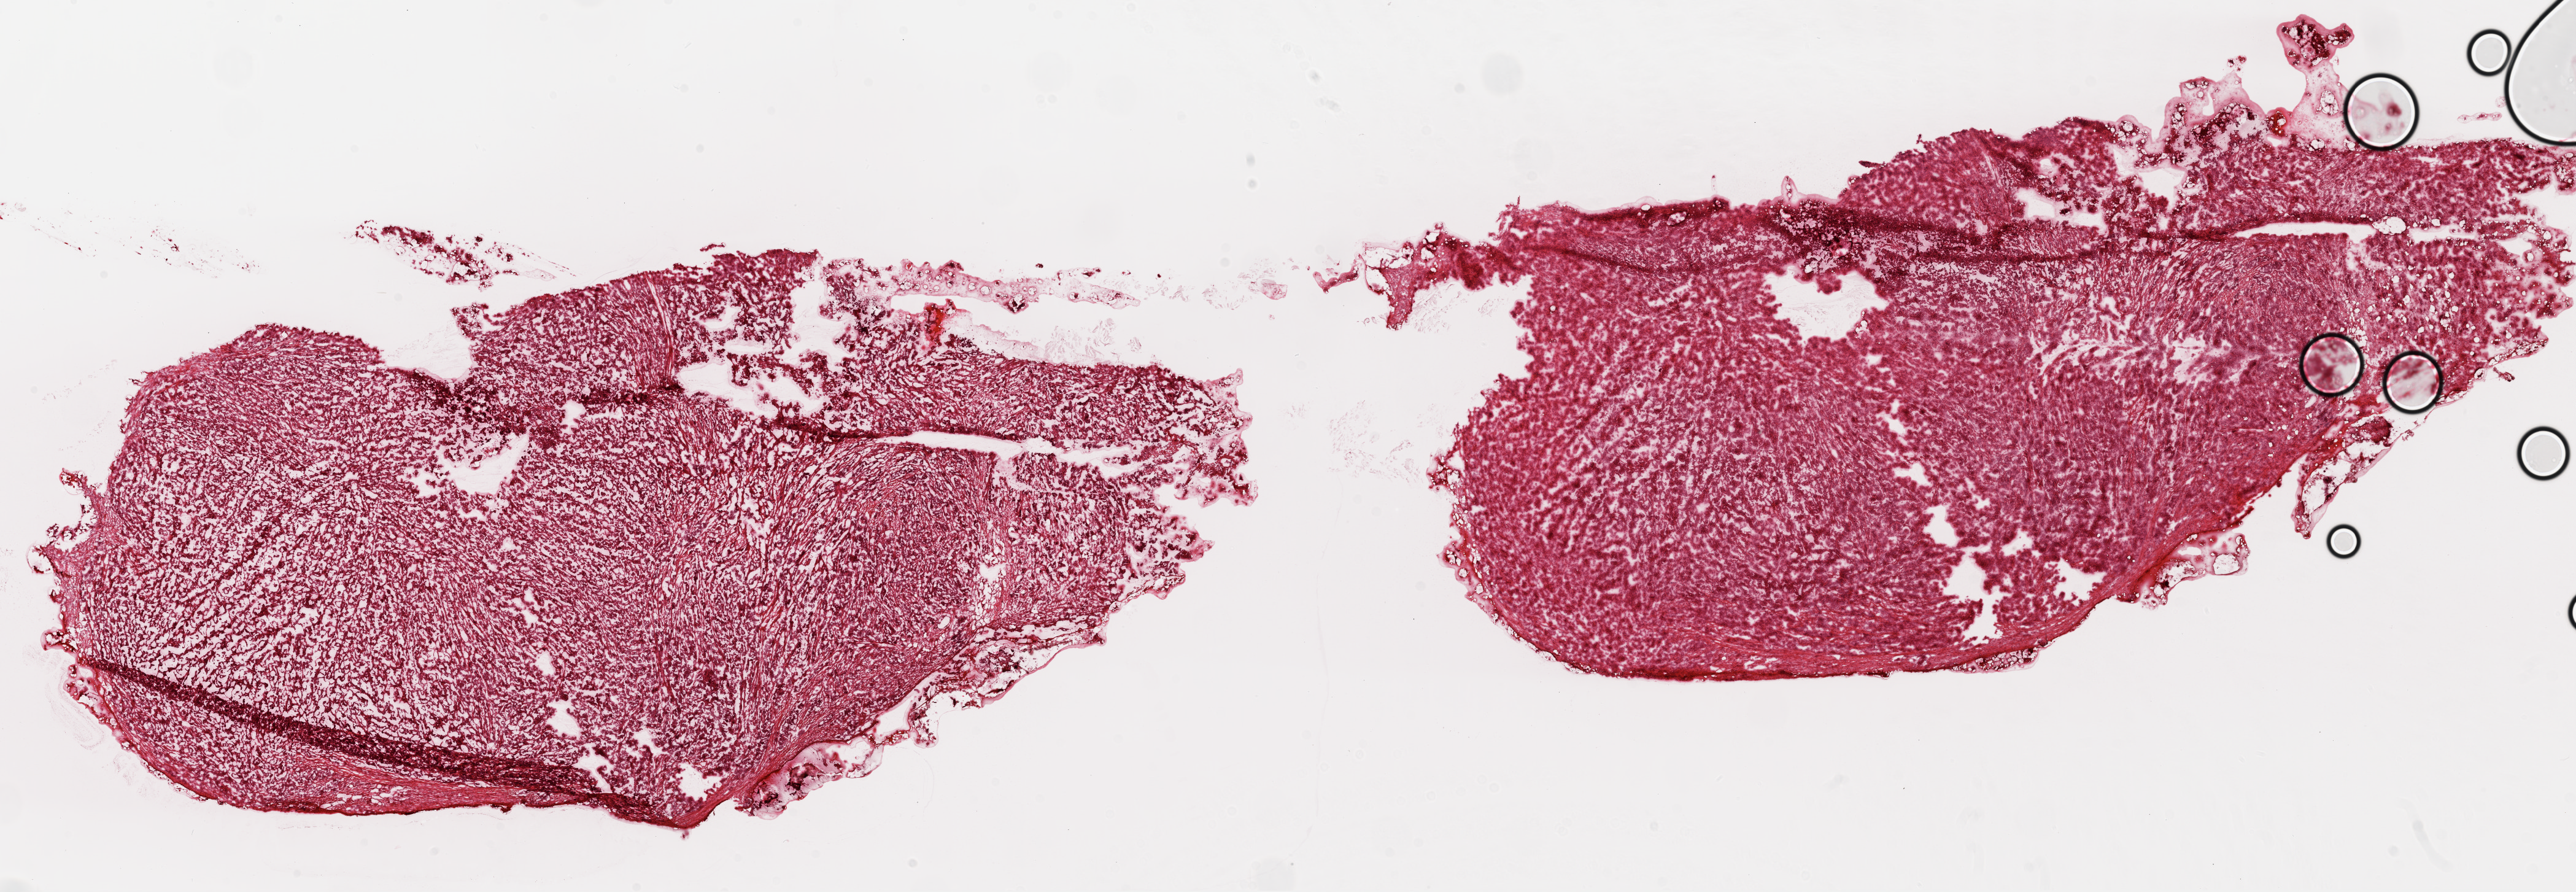
Digitized H&E tissue section (whole slide) — whole scanned area (about 33.8 x 11.7 mm) shown as a low-resolution overview; frozen section; sample: primary tumour, ovary. Female patient; age at initial diagnosis 63 years. Histologic grade: G3 (poorly differentiated). Pathologist review of this section (percent, as recorded): tumour nuclei 95%, normal cells 0%, stromal cells 0%, necrosis 5%.
• FIGO stage: IIIC
• histologic diagnosis: Serous cystadenocarcinoma, NOS